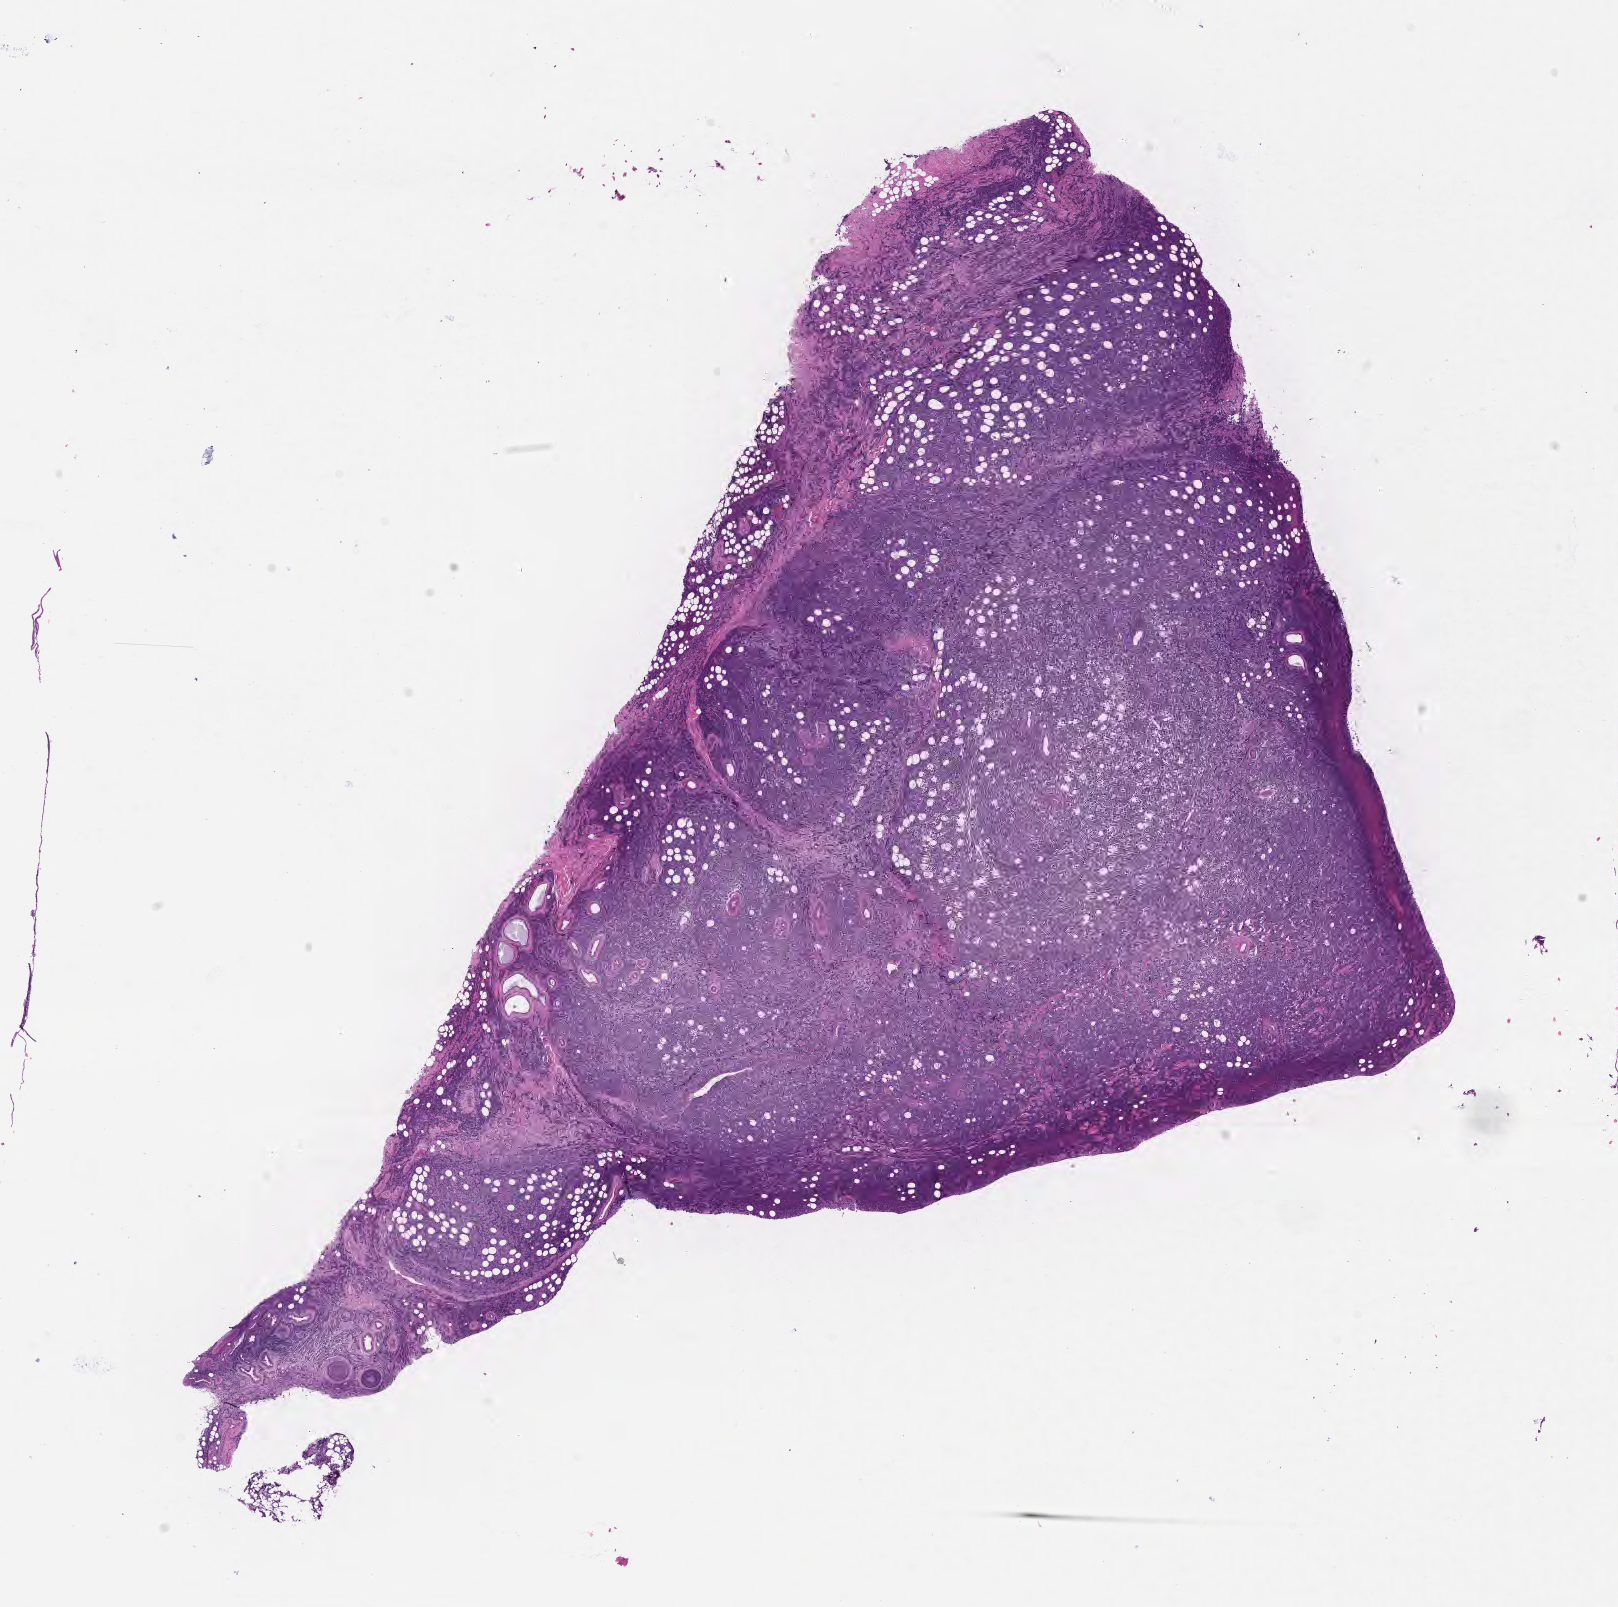
Whole-slide image, haematoxylin and eosin stain — shown as a low-resolution overview of the whole scanned area (about 13.1 x 13.0 mm), FFPE section, primary tumor. Patient male; aged 46. Slide review estimates, as recorded: tumor cells 80%, tumor nuclei 85%, stromal cells 15%, necrosis 5%, normal cells 0%. Inflammatory infiltration, as recorded: lymphocyte infiltration 50%, monocyte infiltration 25%, neutrophil infiltration 5%.
- diagnosis: Burkitt lymphoma, NOS
- Ann Arbor stage (patient): Stage IV